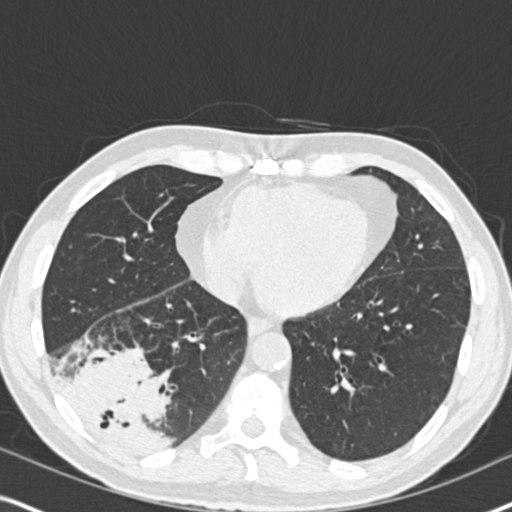
Axial slice from a low-dose chest CT screening exam, second screening round (one year after baseline), lung window (W 1500 / L -600 HU), 2 mm slice thickness. Male participant, aged 61 years at enrolment. Current smoker at enrolment.
Lesion marked by an expert reader, bounding box (x1, y1, x2, y2) in pixels: (45, 318, 188, 462). The exam's reader record, not a measurement of the box and not confirmed to be the same lesion: non-calcified nodule or mass ≥4 mm, right lower lobe, 90 × 80 mm, soft tissue attenuation, pre-existing on the prior screen: yes; interval growth: yes. Official screen result: positive, other. Lung cancer was diagnosed 20 days after this screen: bronchiolo-alveolar adenocarcinoma, NOS, right lower lobe, moderately differentiated (G2), stage IIIB (AJCC 6th edition), 90 mm at pathology.